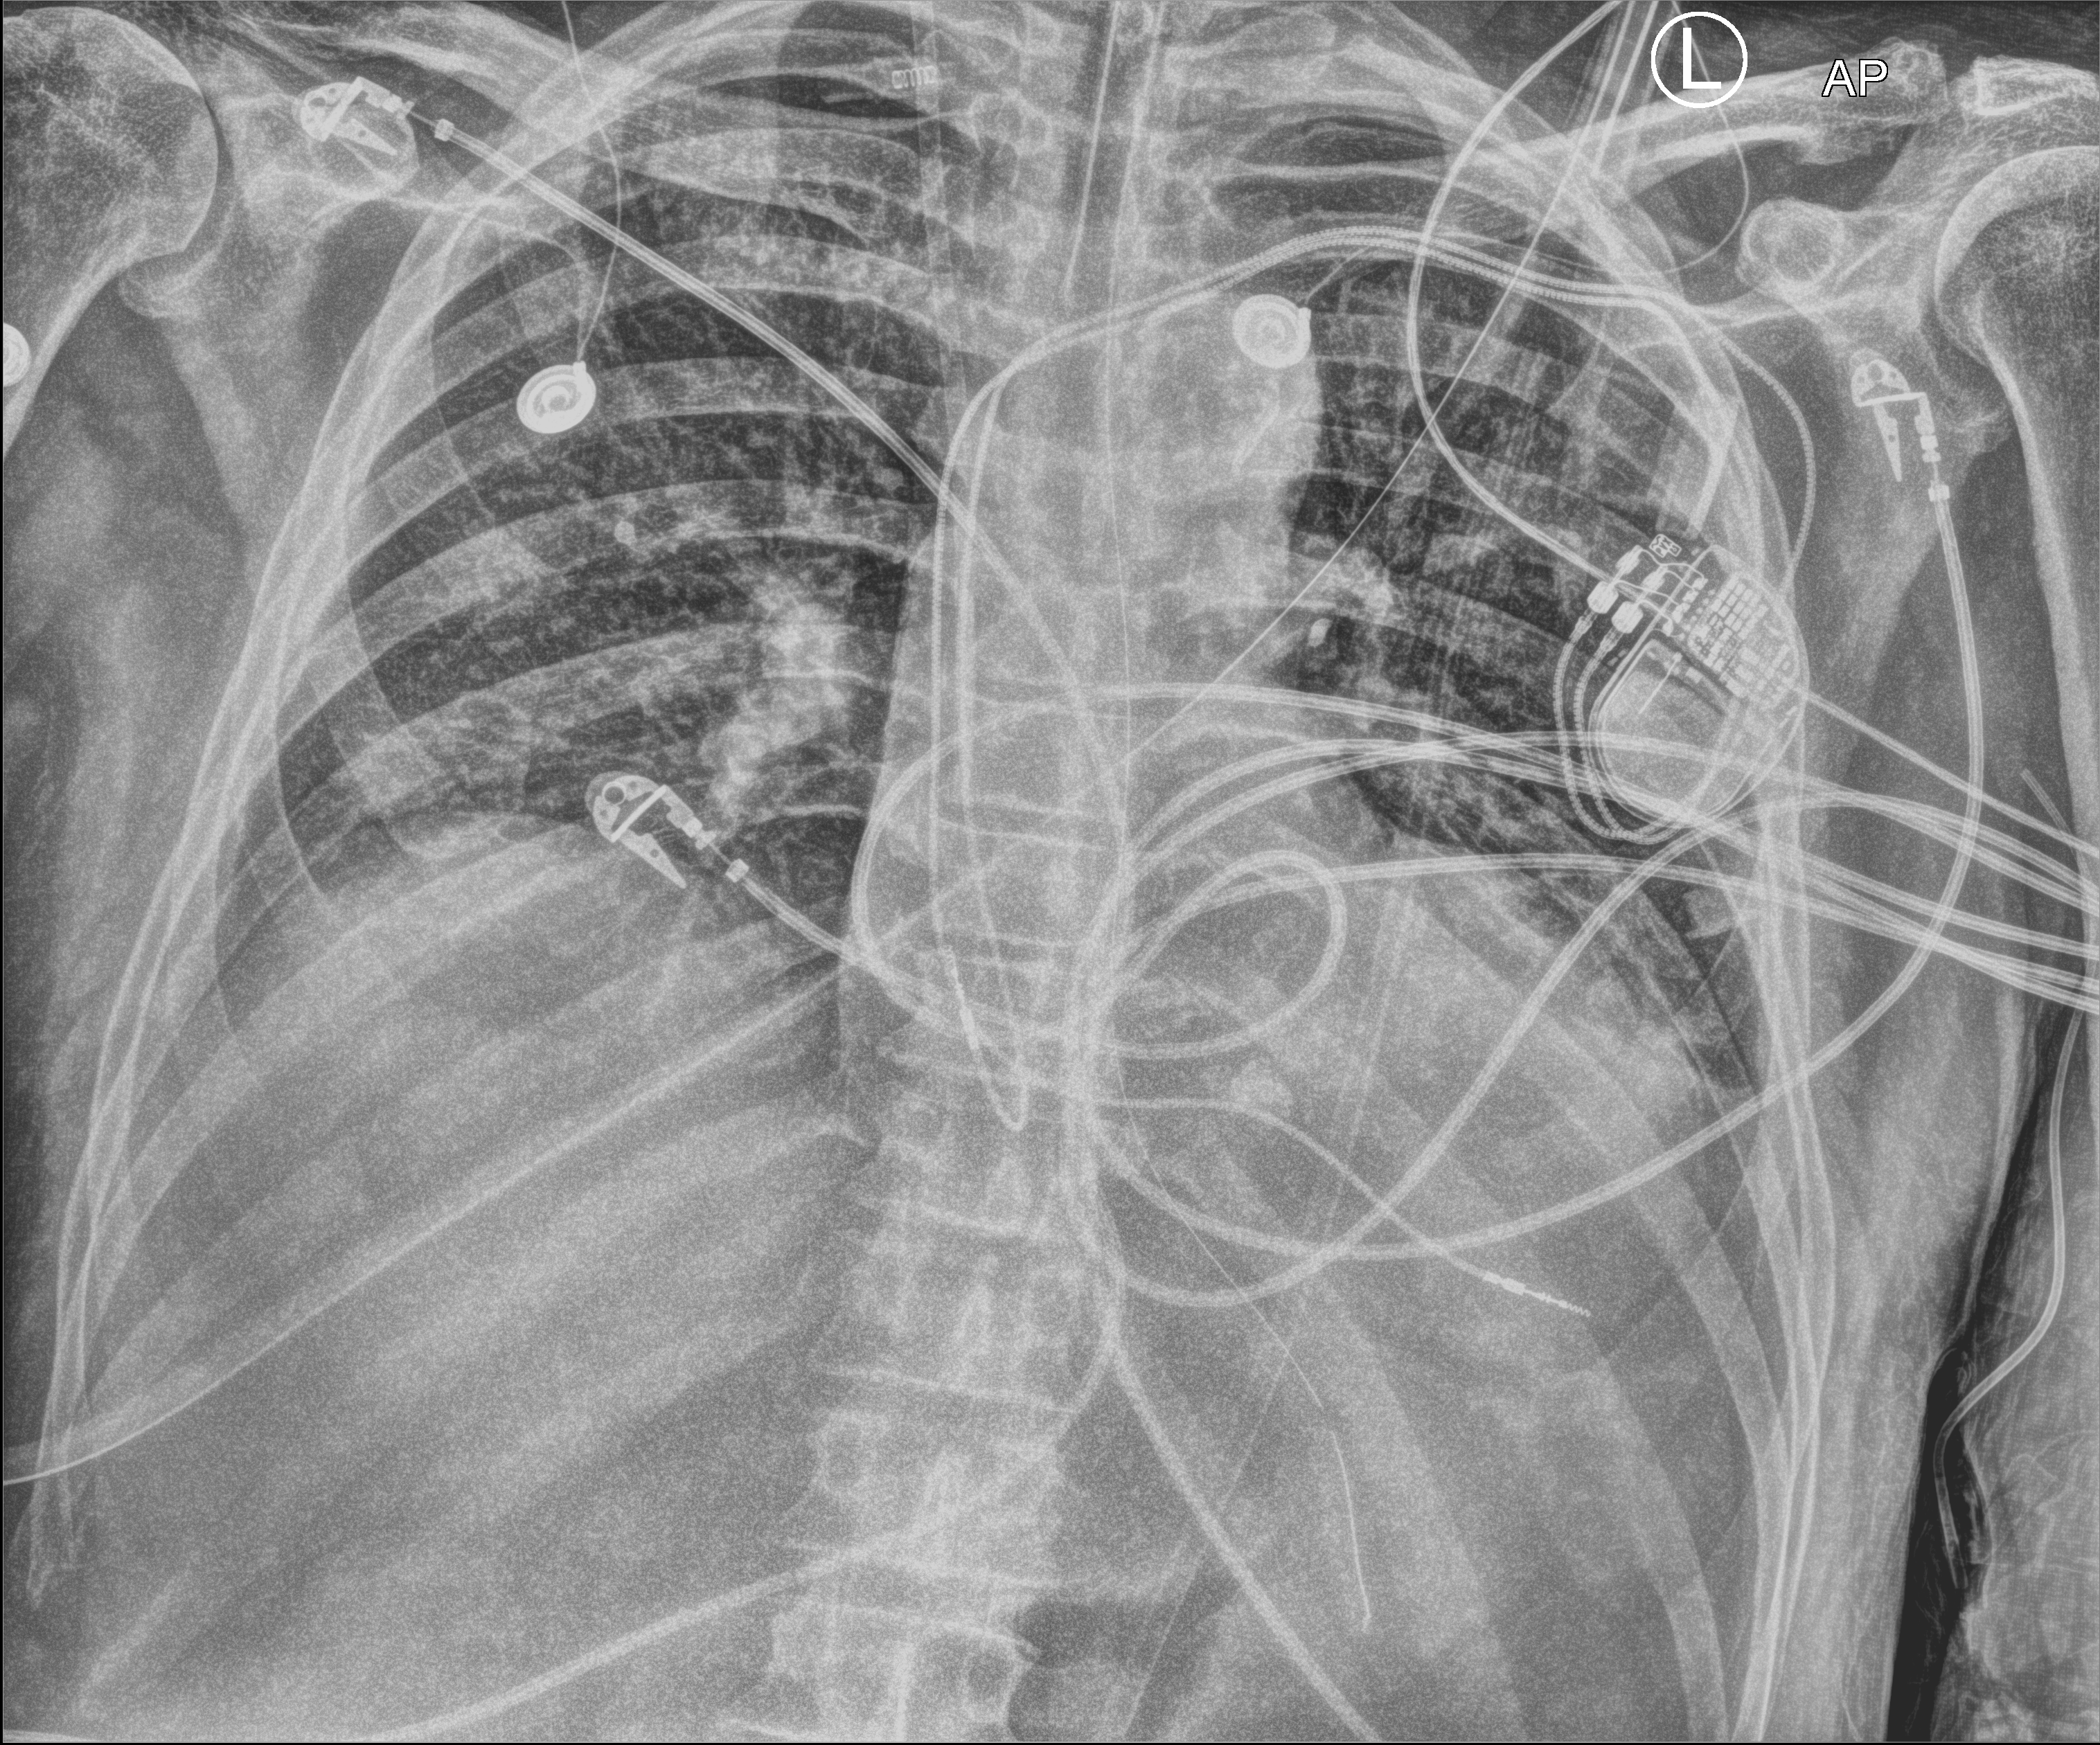
Chest X-ray (portable). Patient hospitalised with COVID-19; male, aged 60–74 years.
Hospital-stay facts (about this admission, not read from this image; timing relative to this image not recorded): mechanically ventilated during this hospital stay: yes; admitted to intensive care during this hospital stay: yes.